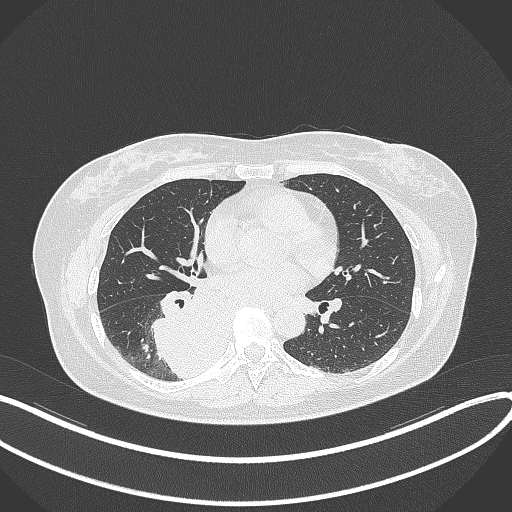
Chest CT, one axial slice. Position 168 of 331 along the scan axis. Reconstruction kernel B70f. Lung window (W 1500 / L -600 HU). 1 mm slice thickness. 512 × 512 image matrix. Patient: female, 54 years. Case-level facts recorded for this patient, not image findings: clinical TNM (as recorded): T4 N0 M0.
Annotated regions visible in this slice (rectangle marked by the reading radiologist):
- lung tumour (recorded histology: adenocarcinoma): bounding box (x1, y1, x2, y2) in pixels: (147, 287, 218, 385)